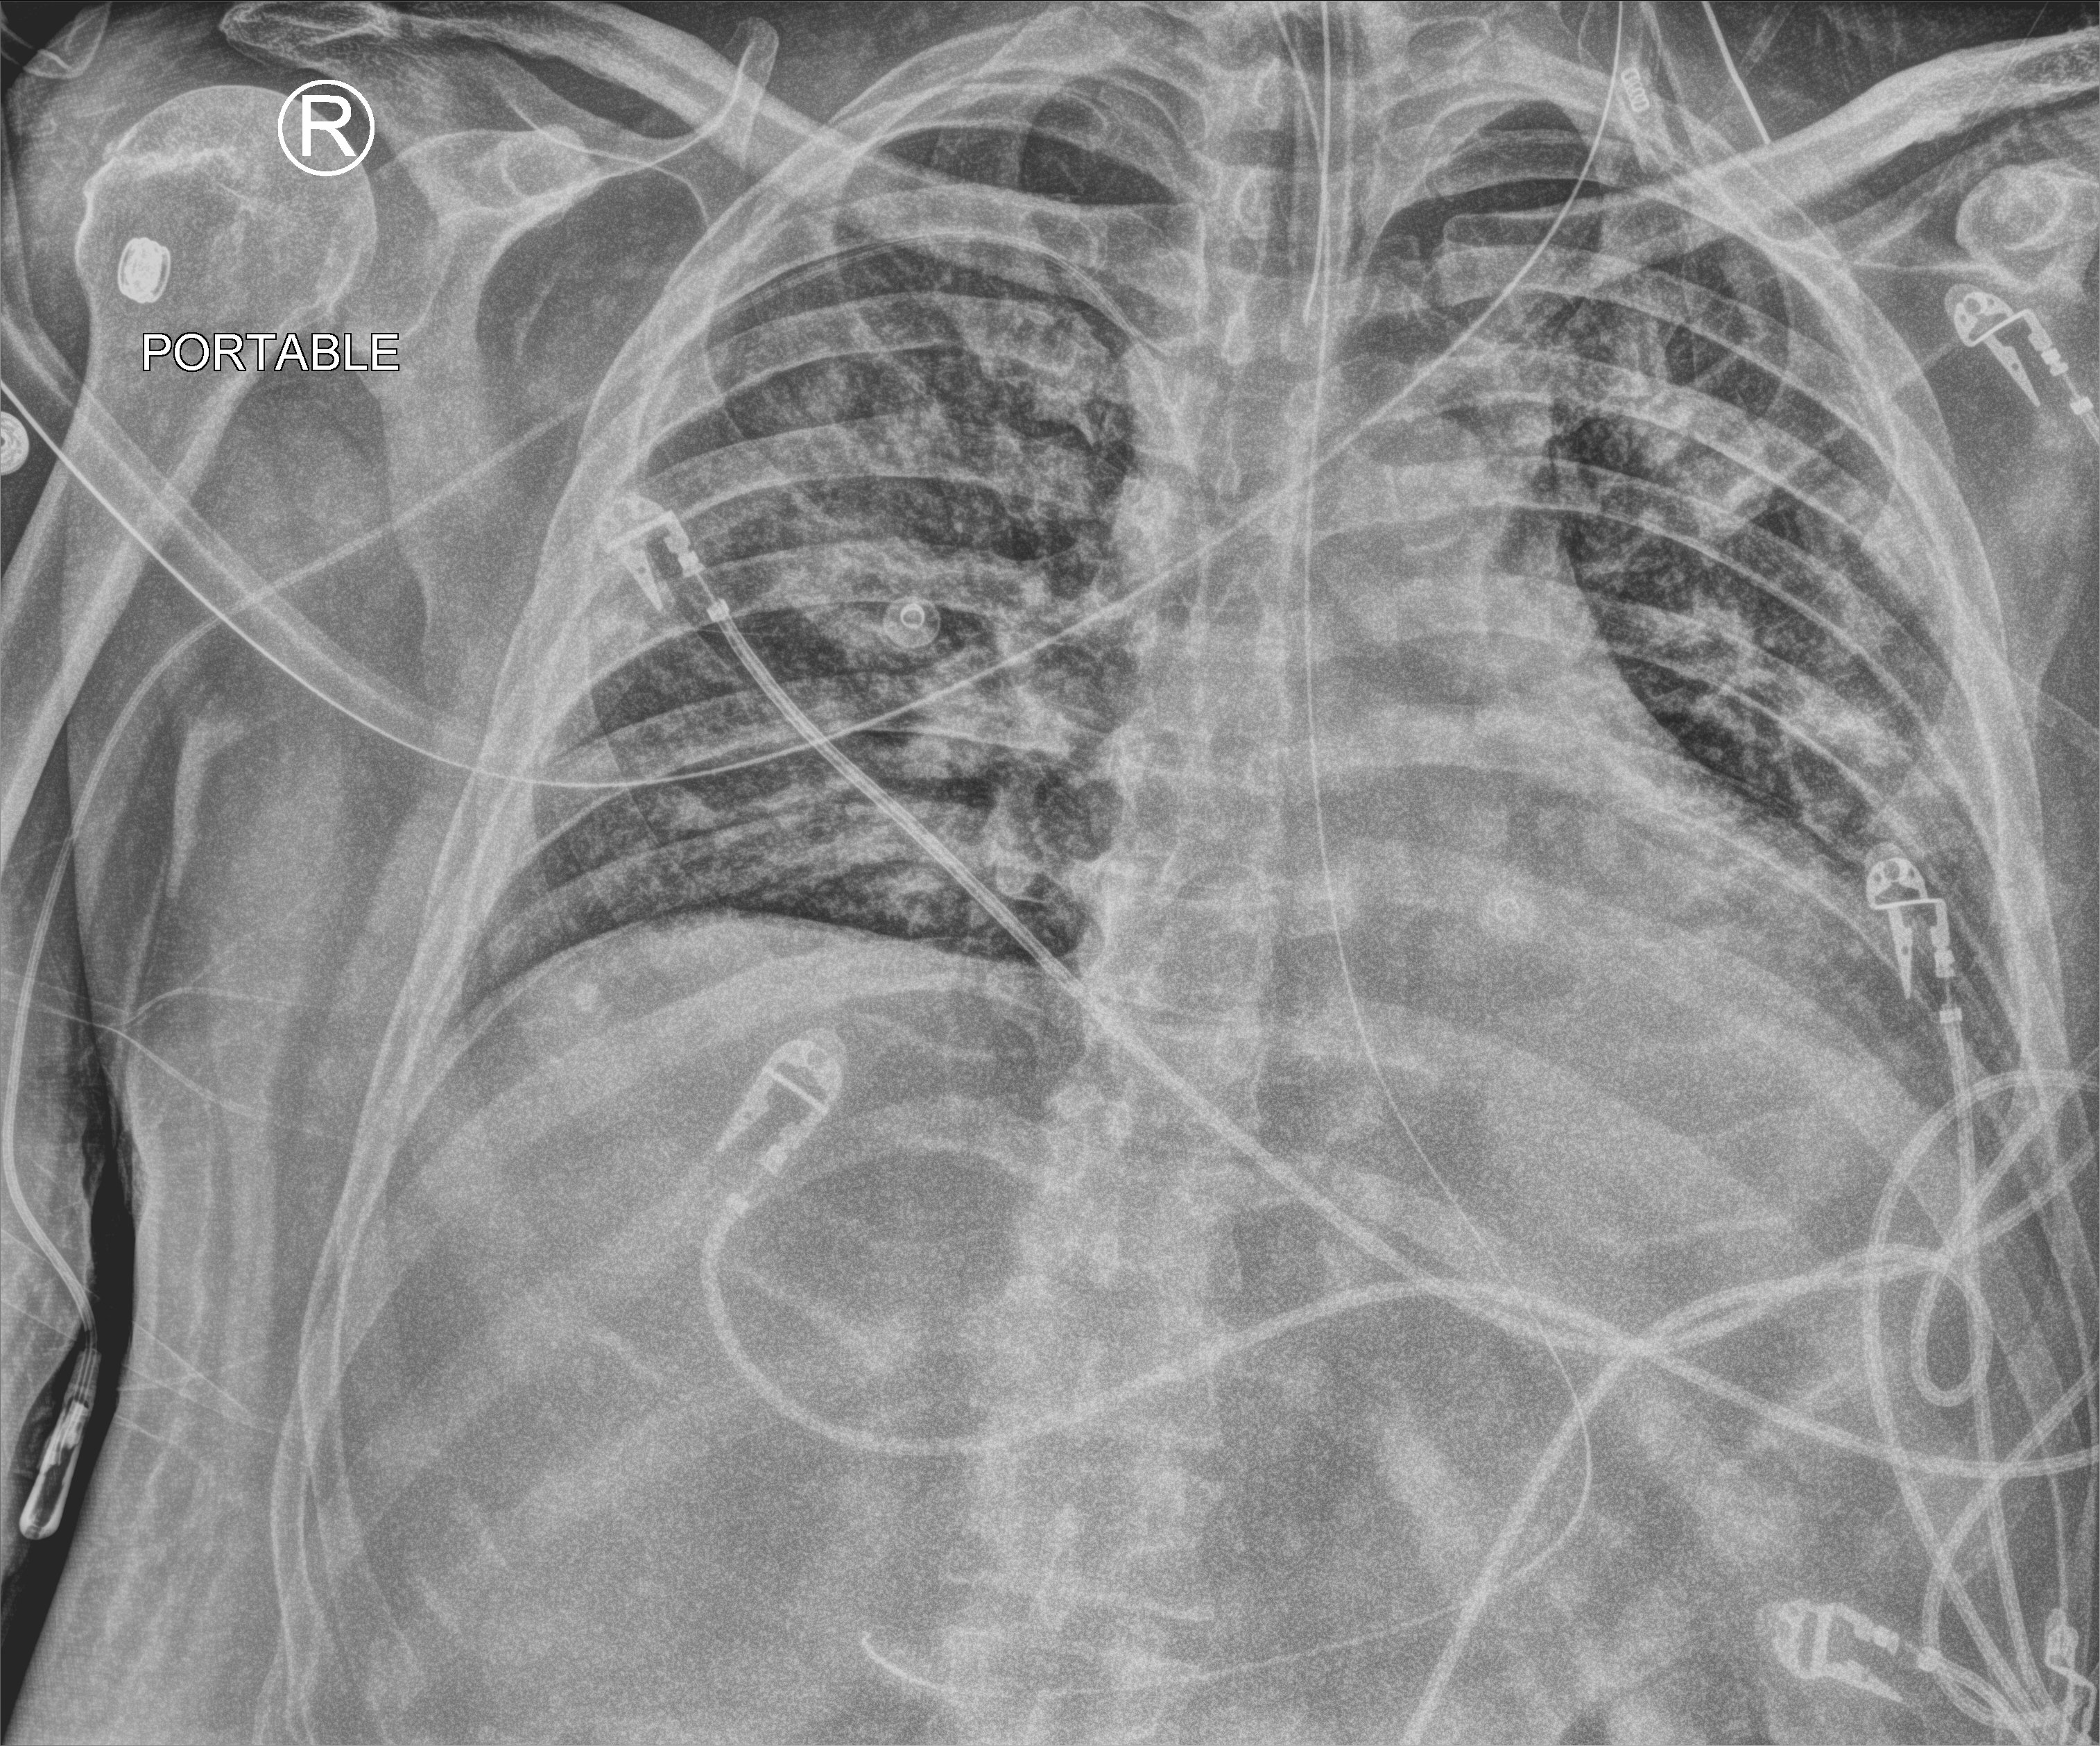
Chest X-ray (portable); anteroposterior (AP) projection. Male patient hospitalised with COVID-19, age 18–59 years.
Hospital-stay facts (about this admission, not read from this image; timing relative to this image not recorded): admitted to intensive care during this hospital stay: yes.